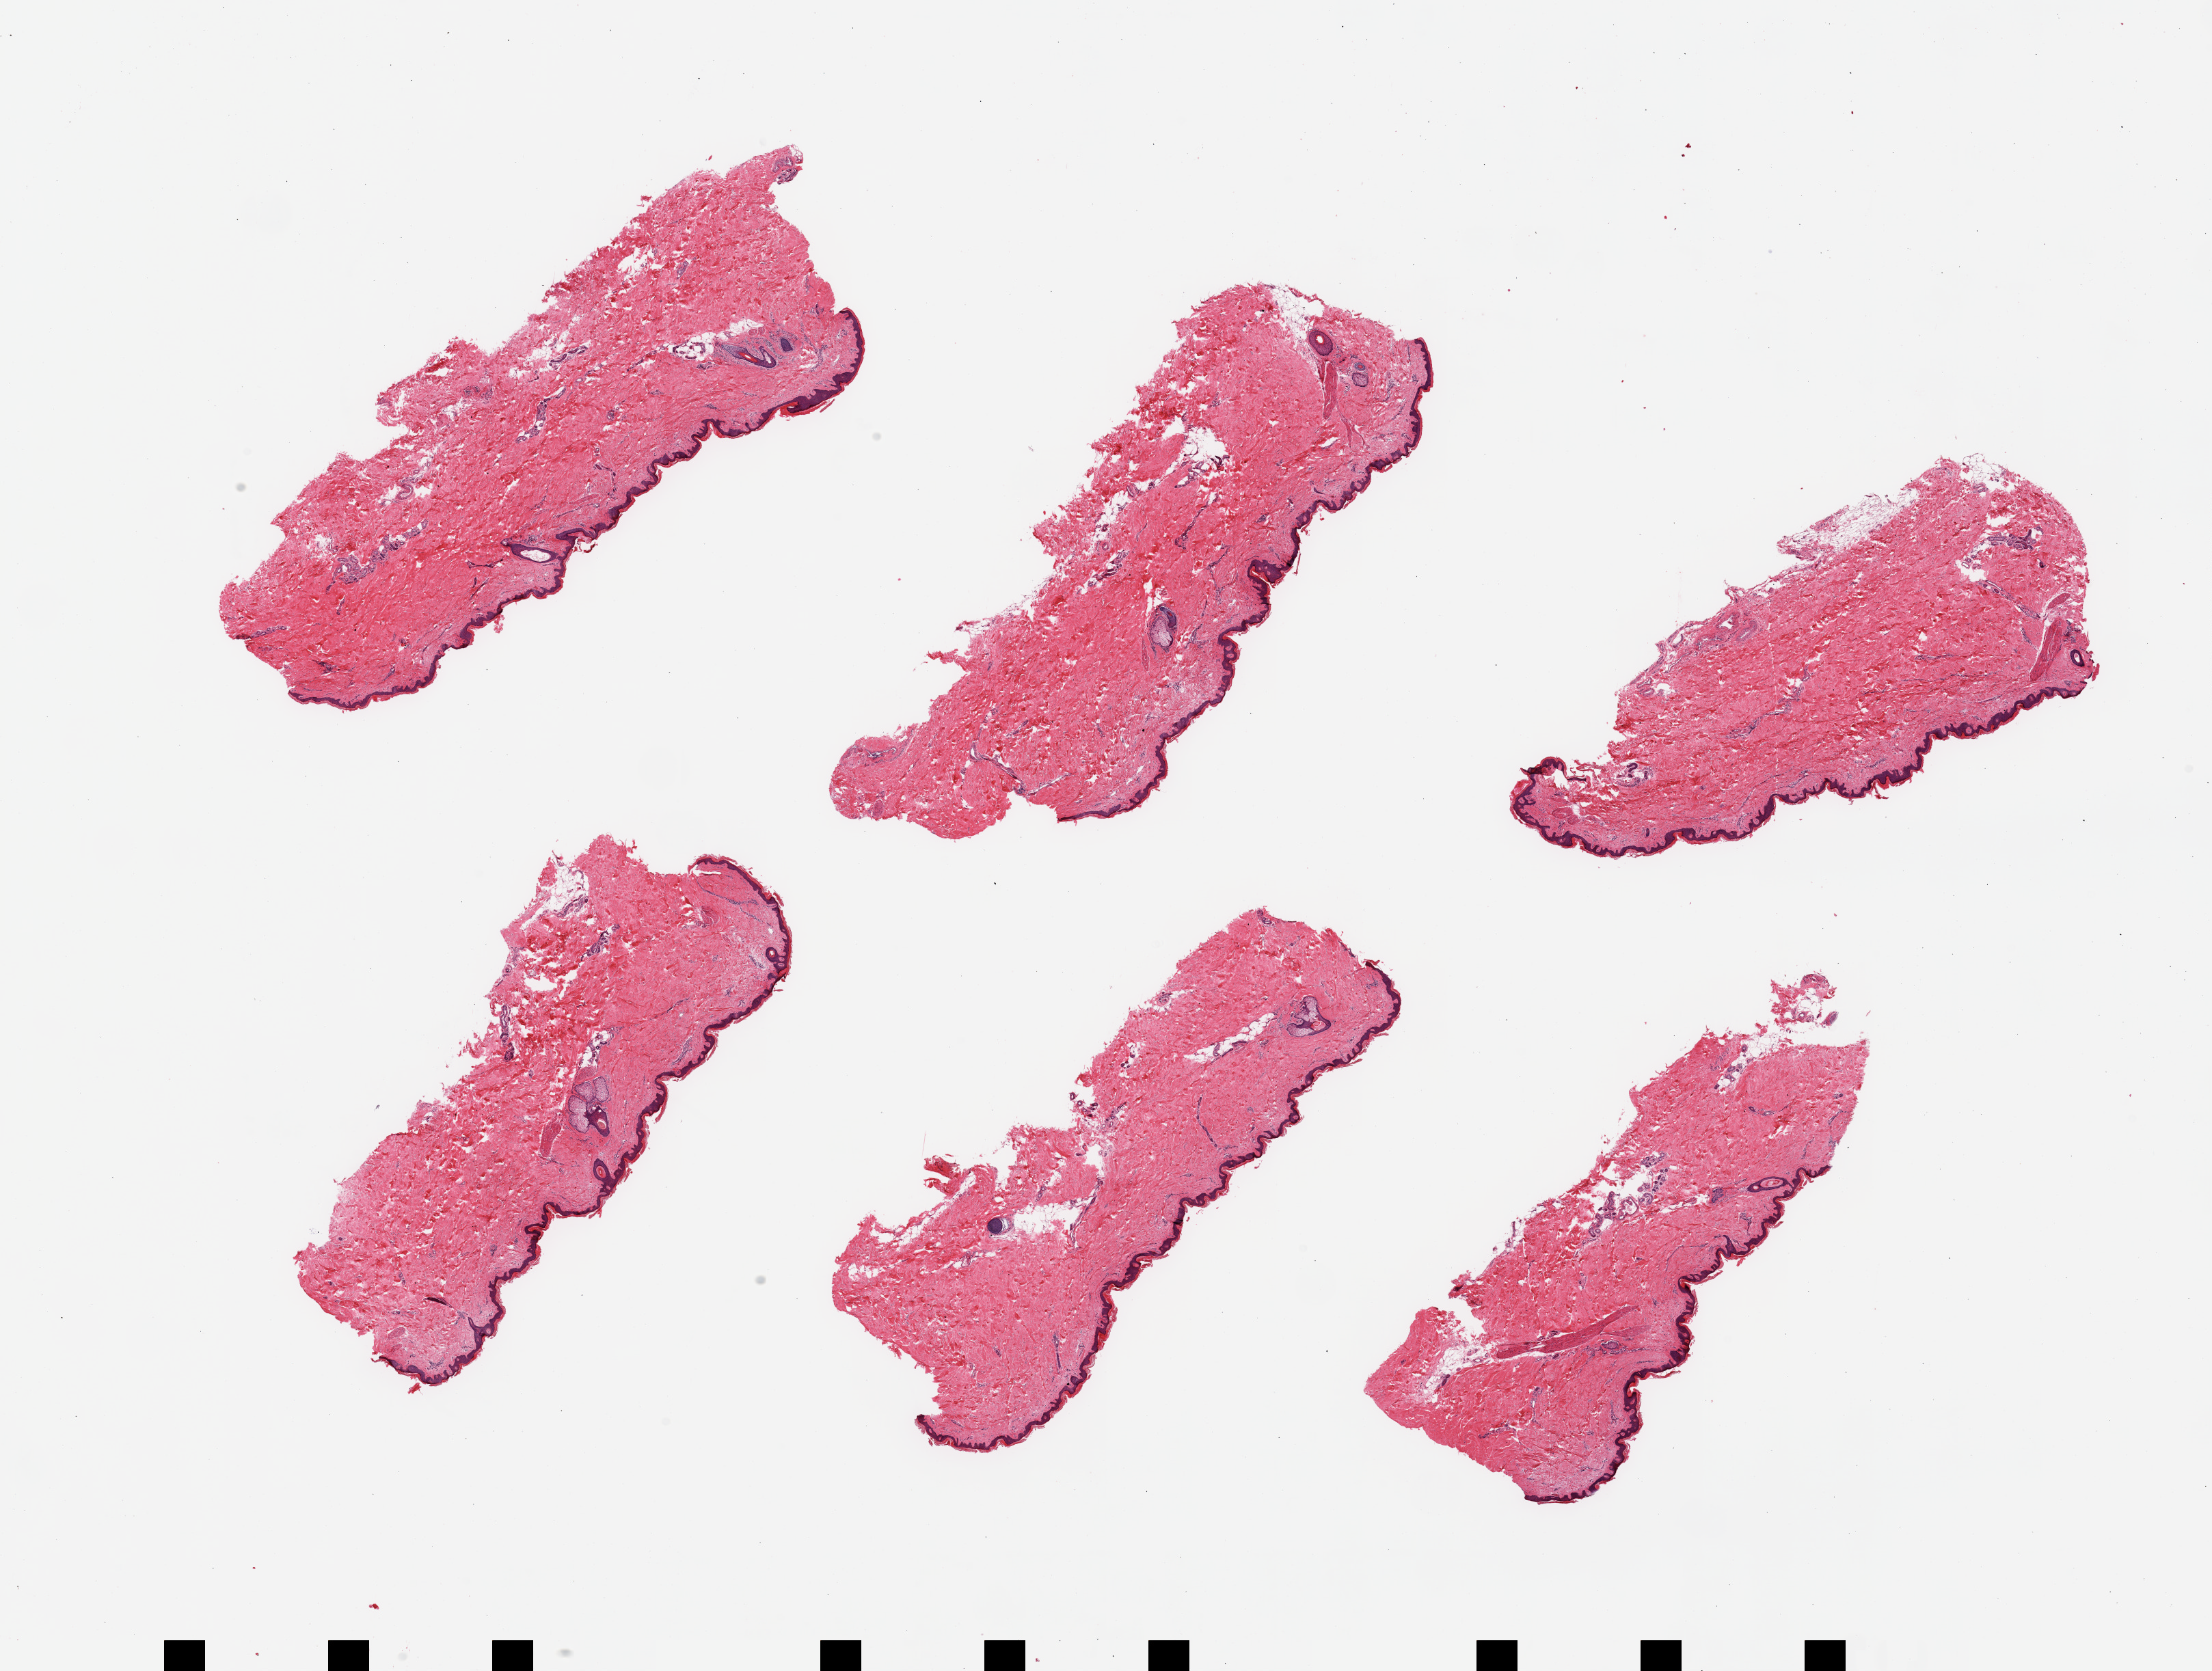
Digitized H&E-stained section, brightfield, shown as a low-resolution overview of the whole scanned area (about 25.6 x 19.3 mm, from a 20x scan), PAXgene-fixed paraffin-embedded (PFPE) section, target tissue: skin of lower leg, donor tissue sample. Donor sex: male.
Reviewer comment on this tissue sample: 6 pieces, squamous epithelium is 30-40microns, minute nubbin adherent dermal fat.